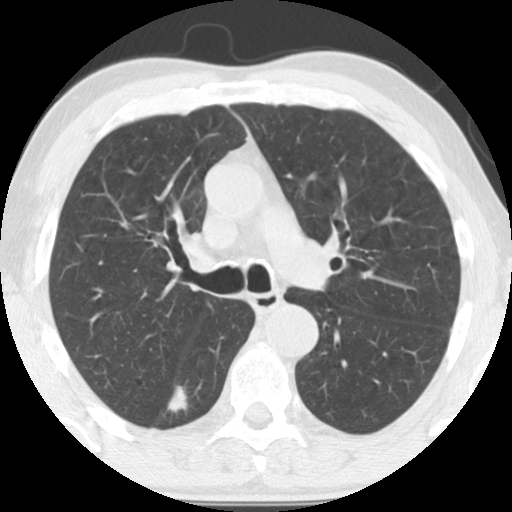
Chest CT (low-dose screening protocol), one axial image; first (baseline) screen; lung window (W 1500 / L -600 HU); 2.5 mm slice thickness; standard (soft-tissue) reconstruction kernel (STANDARD); slice 44 of 135 in the series; 512 × 512 image matrix. Male, age 64 years at enrolment. Current smoker at enrolment.
Expert-annotated lung lesion, bounding box [x1, y1, x2, y2] px = [121, 365, 197, 434]. Screening reader's record for this exam (one nodule recorded; not confirmed to be the boxed lesion): non-calcified nodule or mass ≥4 mm, right lower lobe, 36 × 26 mm, spiculated (stellate) margins, soft tissue attenuation. Lung cancer was diagnosed 20 days after this screen: adenocarcinoma, NOS, right lower lobe, moderately differentiated (G2), stage IA (AJCC 6th edition), 28 mm at pathology.